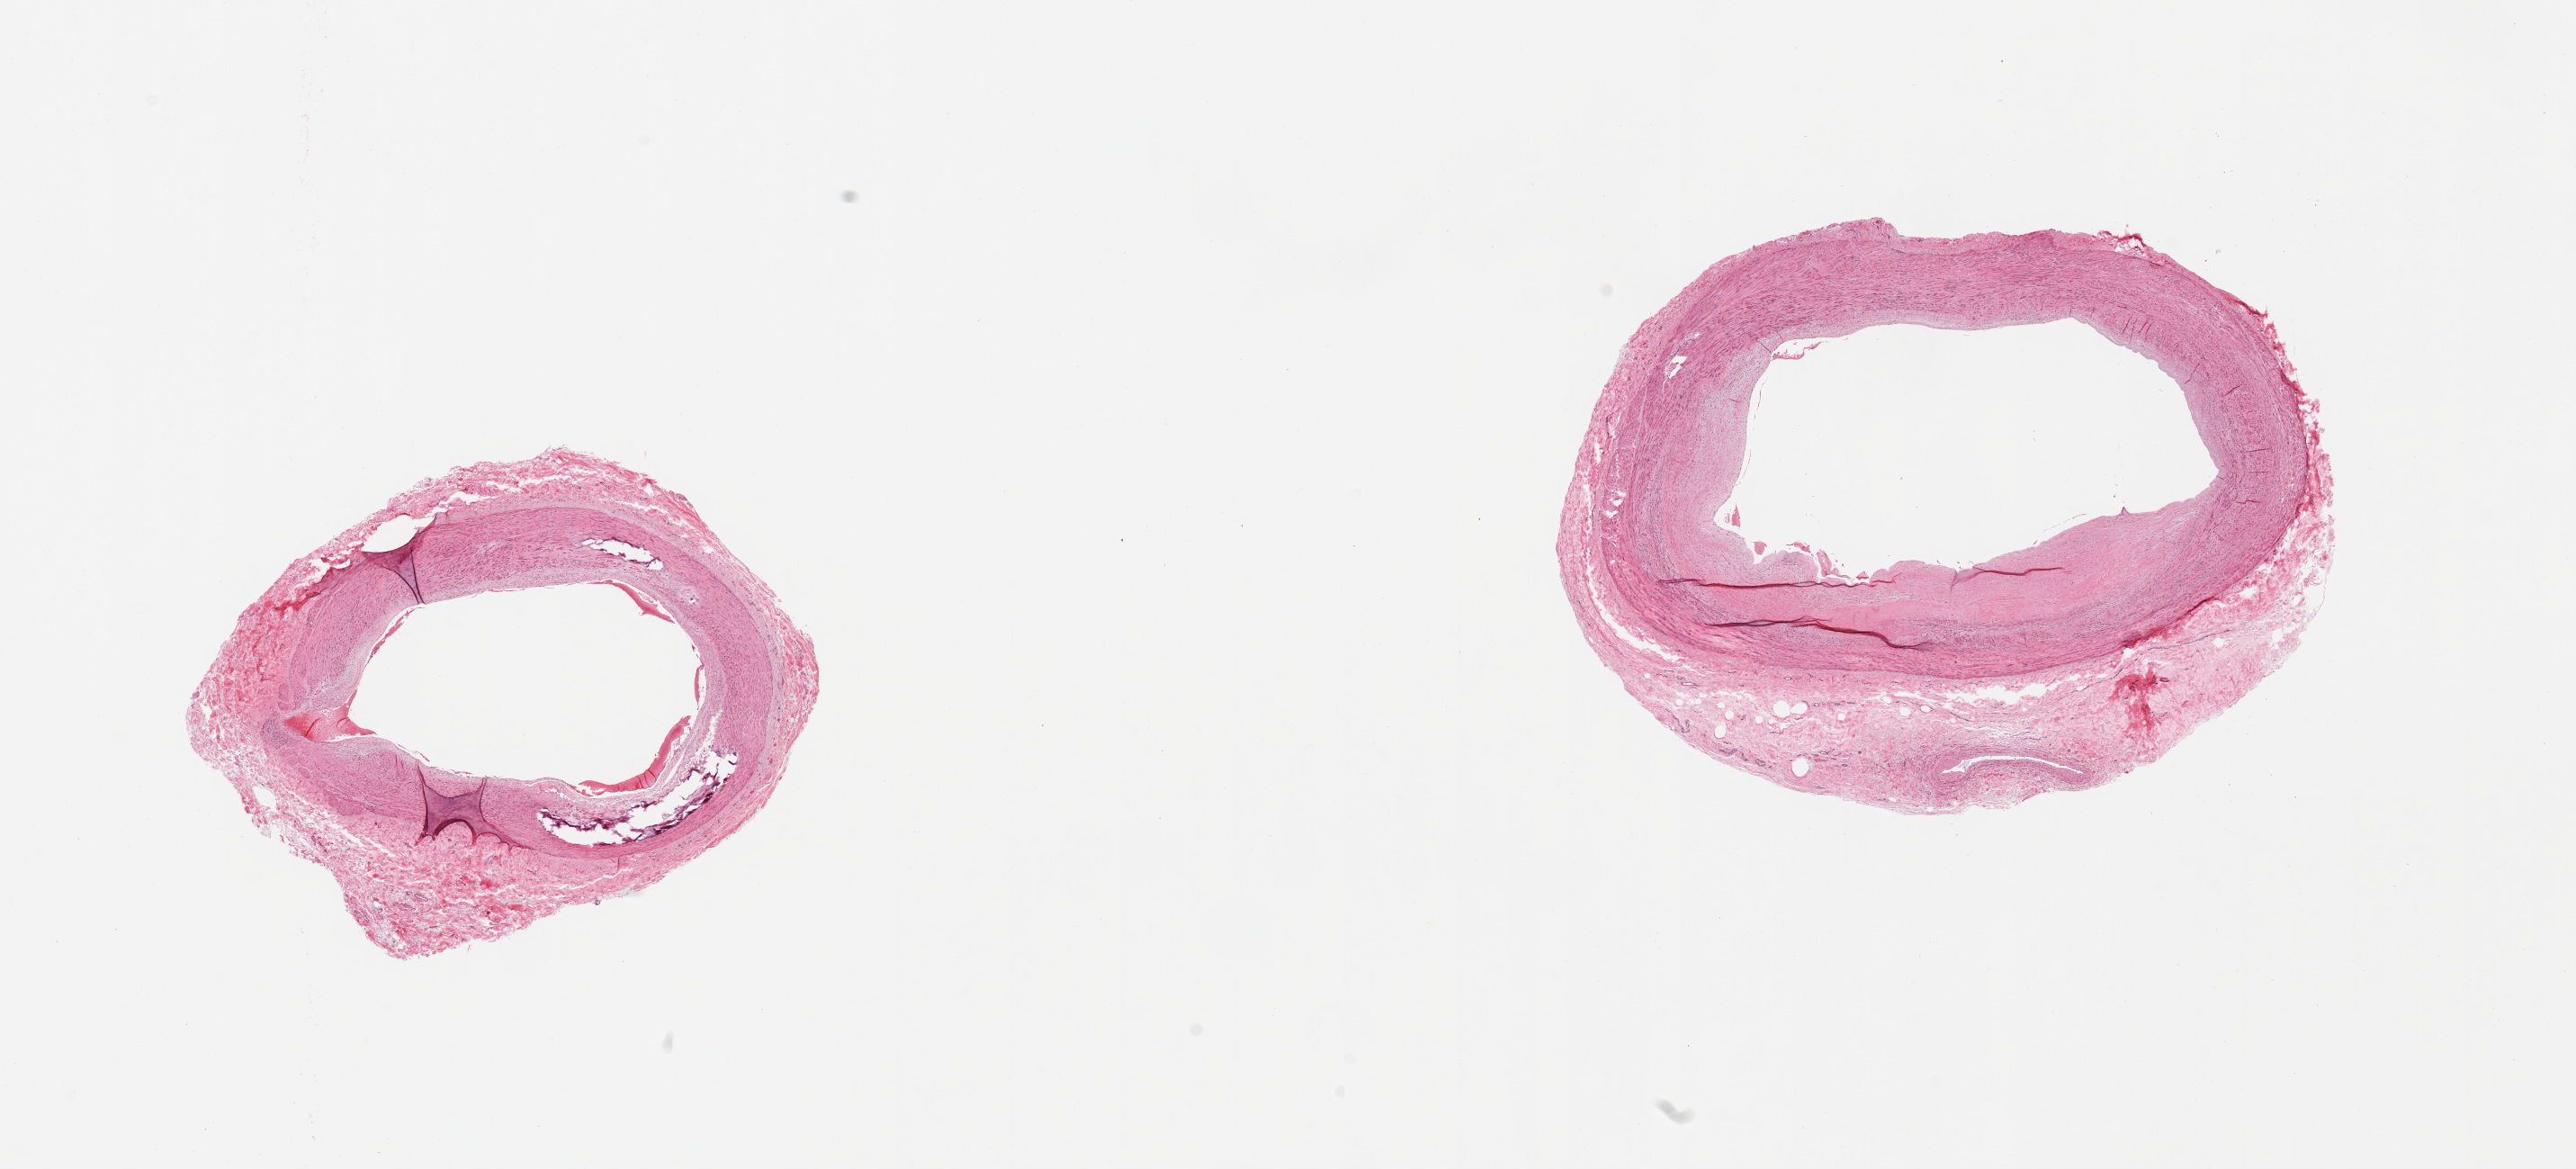
Digitized haematoxylin and eosin-stained section, brightfield, a low-resolution overview of the entire scanned area, about 22.6 x 10.3 mm. PAXgene-fixed paraffin-embedded (PFPE) section. Target tissue: tibial artery. Donor tissue sample. Male donor.
Review note (as recorded): 2 pieces, ~10% occlusive atherosis; Monckeberg medial sclerosis; adherent rims of fibrous tissue up to ~1mm.